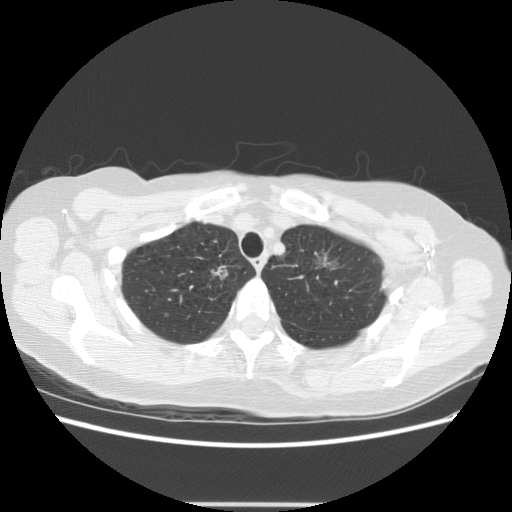
Axial slice from a low-dose chest CT screening exam, third annual screen, lung window (W 1500 / L -600 HU), 2.5 mm slice thickness, slice 106 of 126 in the series. Female participant, aged 65 years at enrolment. Former smoker at enrolment.
Lesion marked by an expert reader, bounding box <291,231,366,294> (left, top, right, bottom; pixels). The exam's reader record, not a measurement of the box and not confirmed to be the same lesion: non-calcified nodule or mass ≥4 mm, left upper lobe, 17 × 14 mm, poorly defined margins, ground glass attenuation, pre-existing on the prior screen: yes; interval growth: yes. Participant outcome: lung cancer diagnosed 96 days after this screen — adenocarcinoma, NOS, left upper lobe, moderately differentiated (G2), stage IA (AJCC 6th edition), 30 mm at pathology.